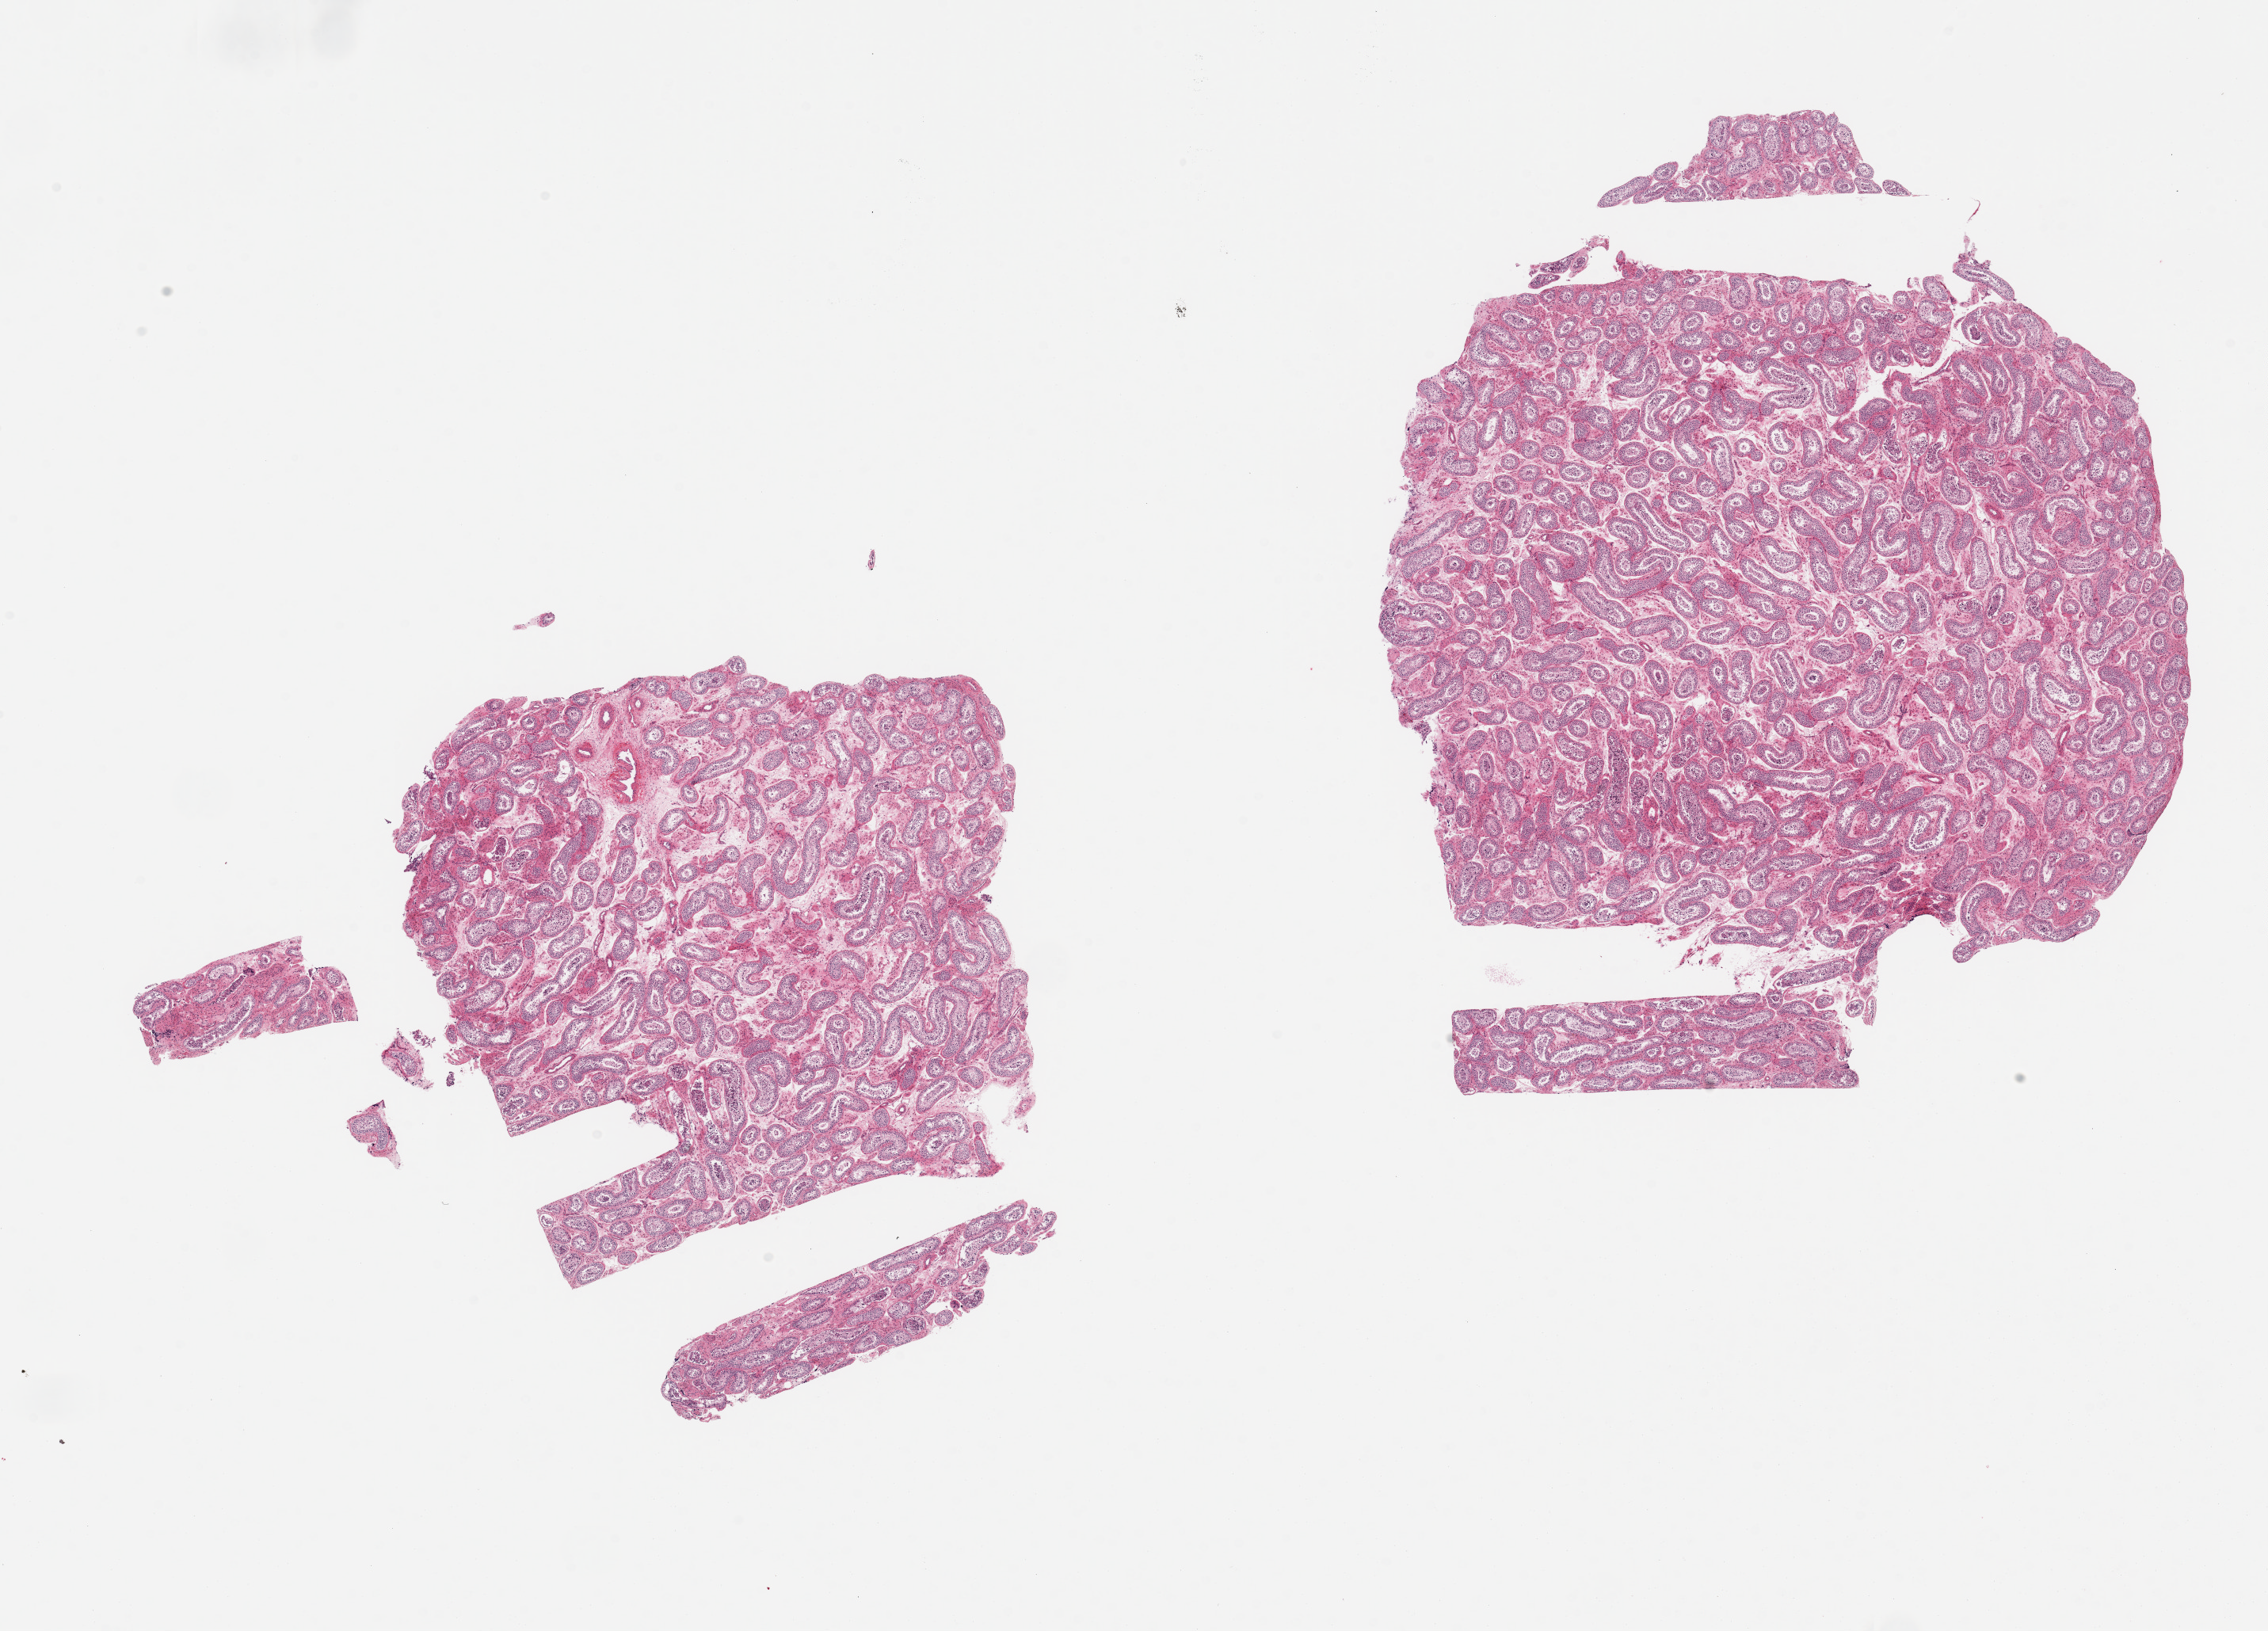
Digitized hematoxylin and eosin (H&E)-stained section, low-resolution overview of the scanned area, about 22.6 x 16.3 mm (slide scanned at 20x). PAXgene-fixed paraffin-embedded (PFPE) section. Section of testis (target tissue). Tissue donor sample. Donor sex: male.
Review note (as recorded): 2 pieces; spermatogenesis is present.